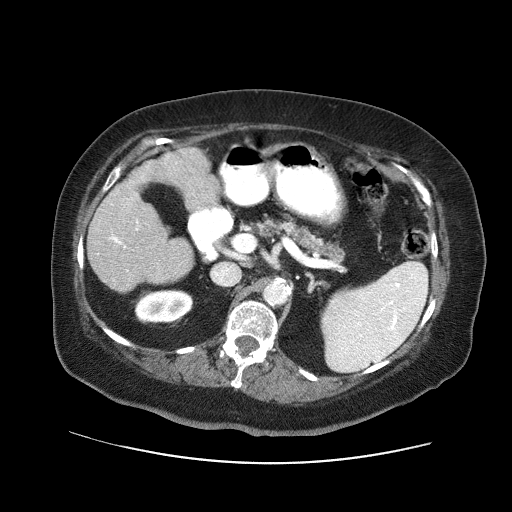
Contrast-enhanced abdominal CT (liver protocol), one axial slice. Slice 20 of 71 in the series (ordered by position). 120 kVp. Soft-tissue window (W 400 / L 40 HU). 2.5 mm slice thickness. 512 × 512 image matrix, field of view 400 × 400 mm. From the clinical record (not read from this slice): diagnosis: hepatocellular carcinoma (patient treated with transarterial chemoembolisation; whether this scan precedes or follows treatment is not stated here); TNM stage (as recorded): Stage-II; Child-Pugh class: A; tumour differentiation: poorly differentiated; tumour nodularity: multinodular.
Annotated regions visible in this slice (semi-automatic segmentation, software-assisted and operator-edited):
- liver parenchyma outside the tumour (the mass and vessels are separate outlines, so this box may not span the whole liver): box from (x=88, y=148) to (x=218, y=292) px
- liver vessels: (x=110, y=220)–(x=138, y=245)